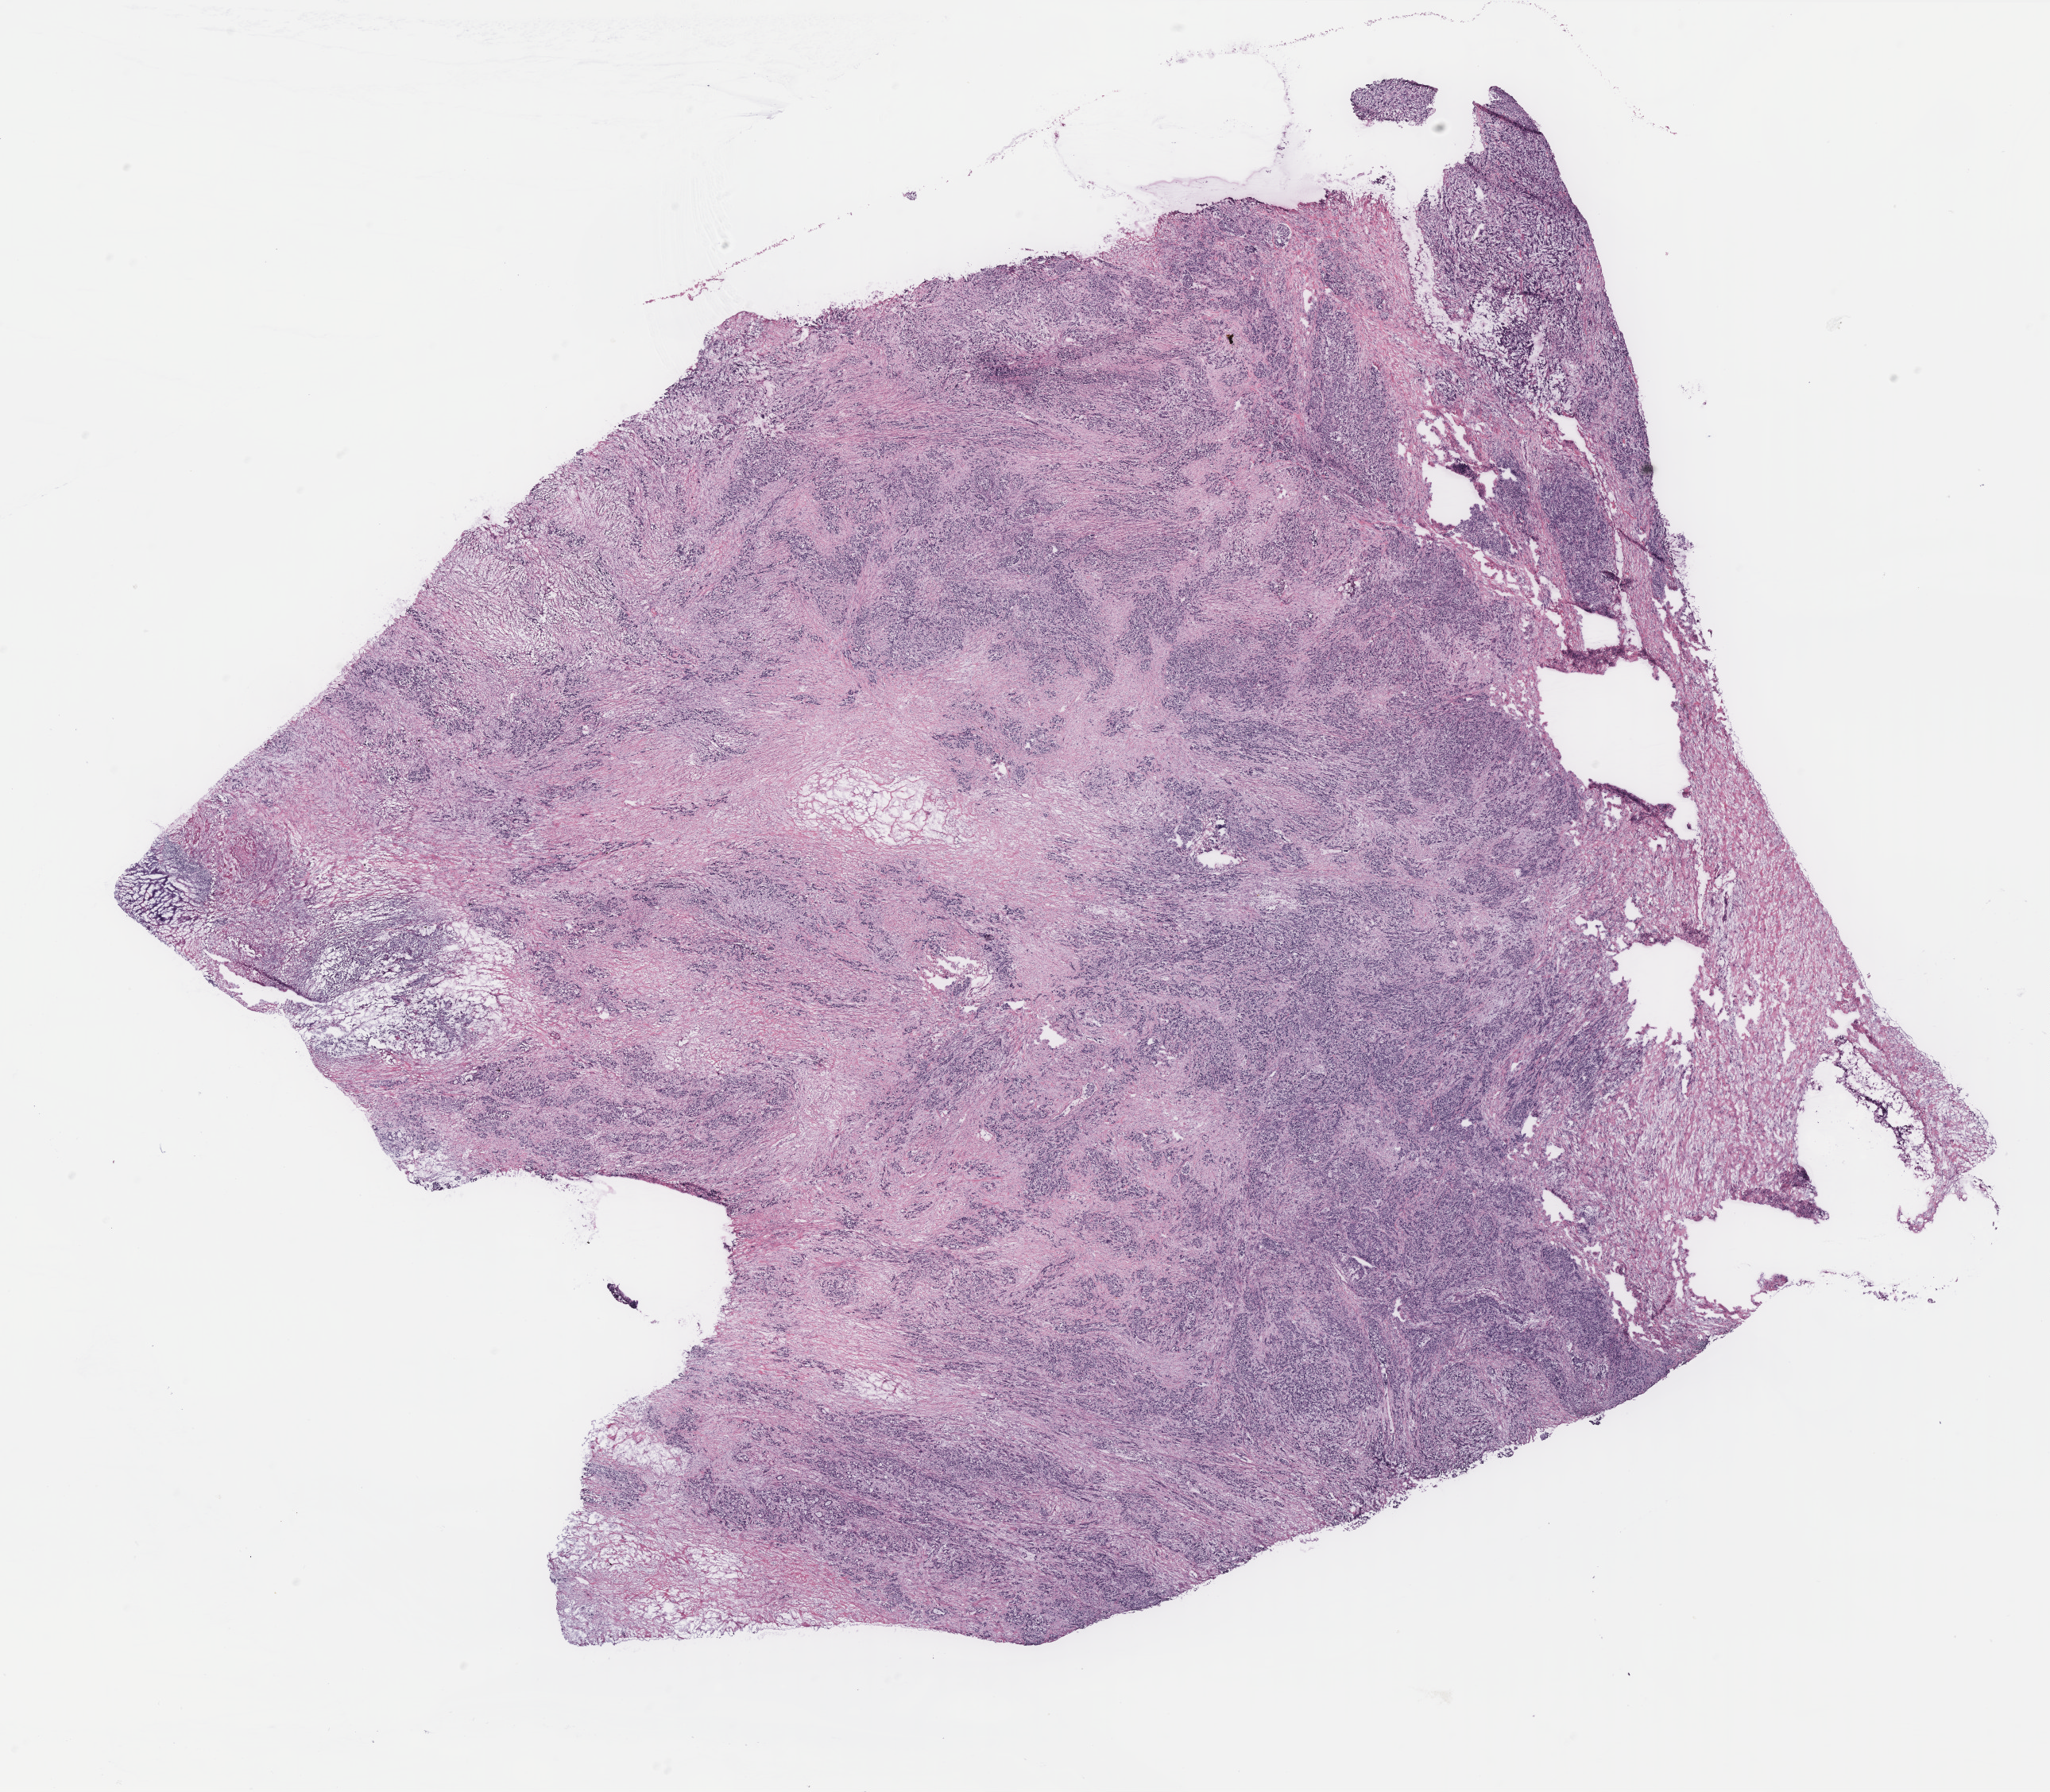
Whole-slide histology image, Hematoxylin and eosin (H&E) stained, whole scanned area (about 20.6 x 18.0 mm) shown as a low-resolution overview. Colon, tissue type not recorded.
Patient diagnosis (cohort enrolment): colon cancer (colon).